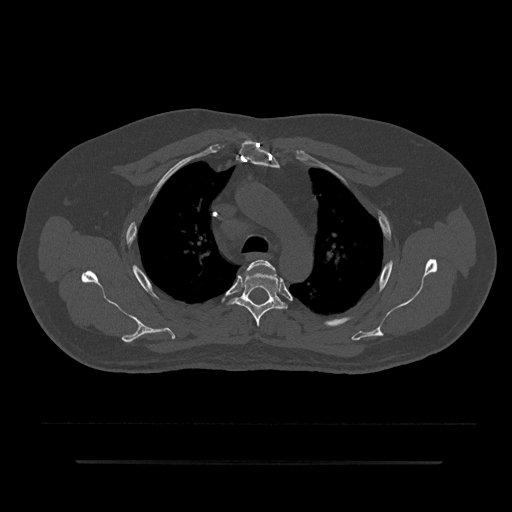
CT including the spine, one axial slice. Slice 621 of 797 in the series (ordered by position). Reconstruction kernel Br40s/3. 120 kVp. Bone window (W 1800 / L 400 HU). 0.5 mm slice thickness. 512 × 512 image matrix, field of view 464 × 464 mm. Male patient, age 59 years. From the clinical record (not read from this slice): primary cancer: bile ducts.
Structures marked on this image (semi-automatic segmentation, software-assisted and operator-edited):
- T3 vertebra: bounding box <246,260,276,275> (left, top, right, bottom; pixels)
- T4 vertebra: <228,269,287,327>